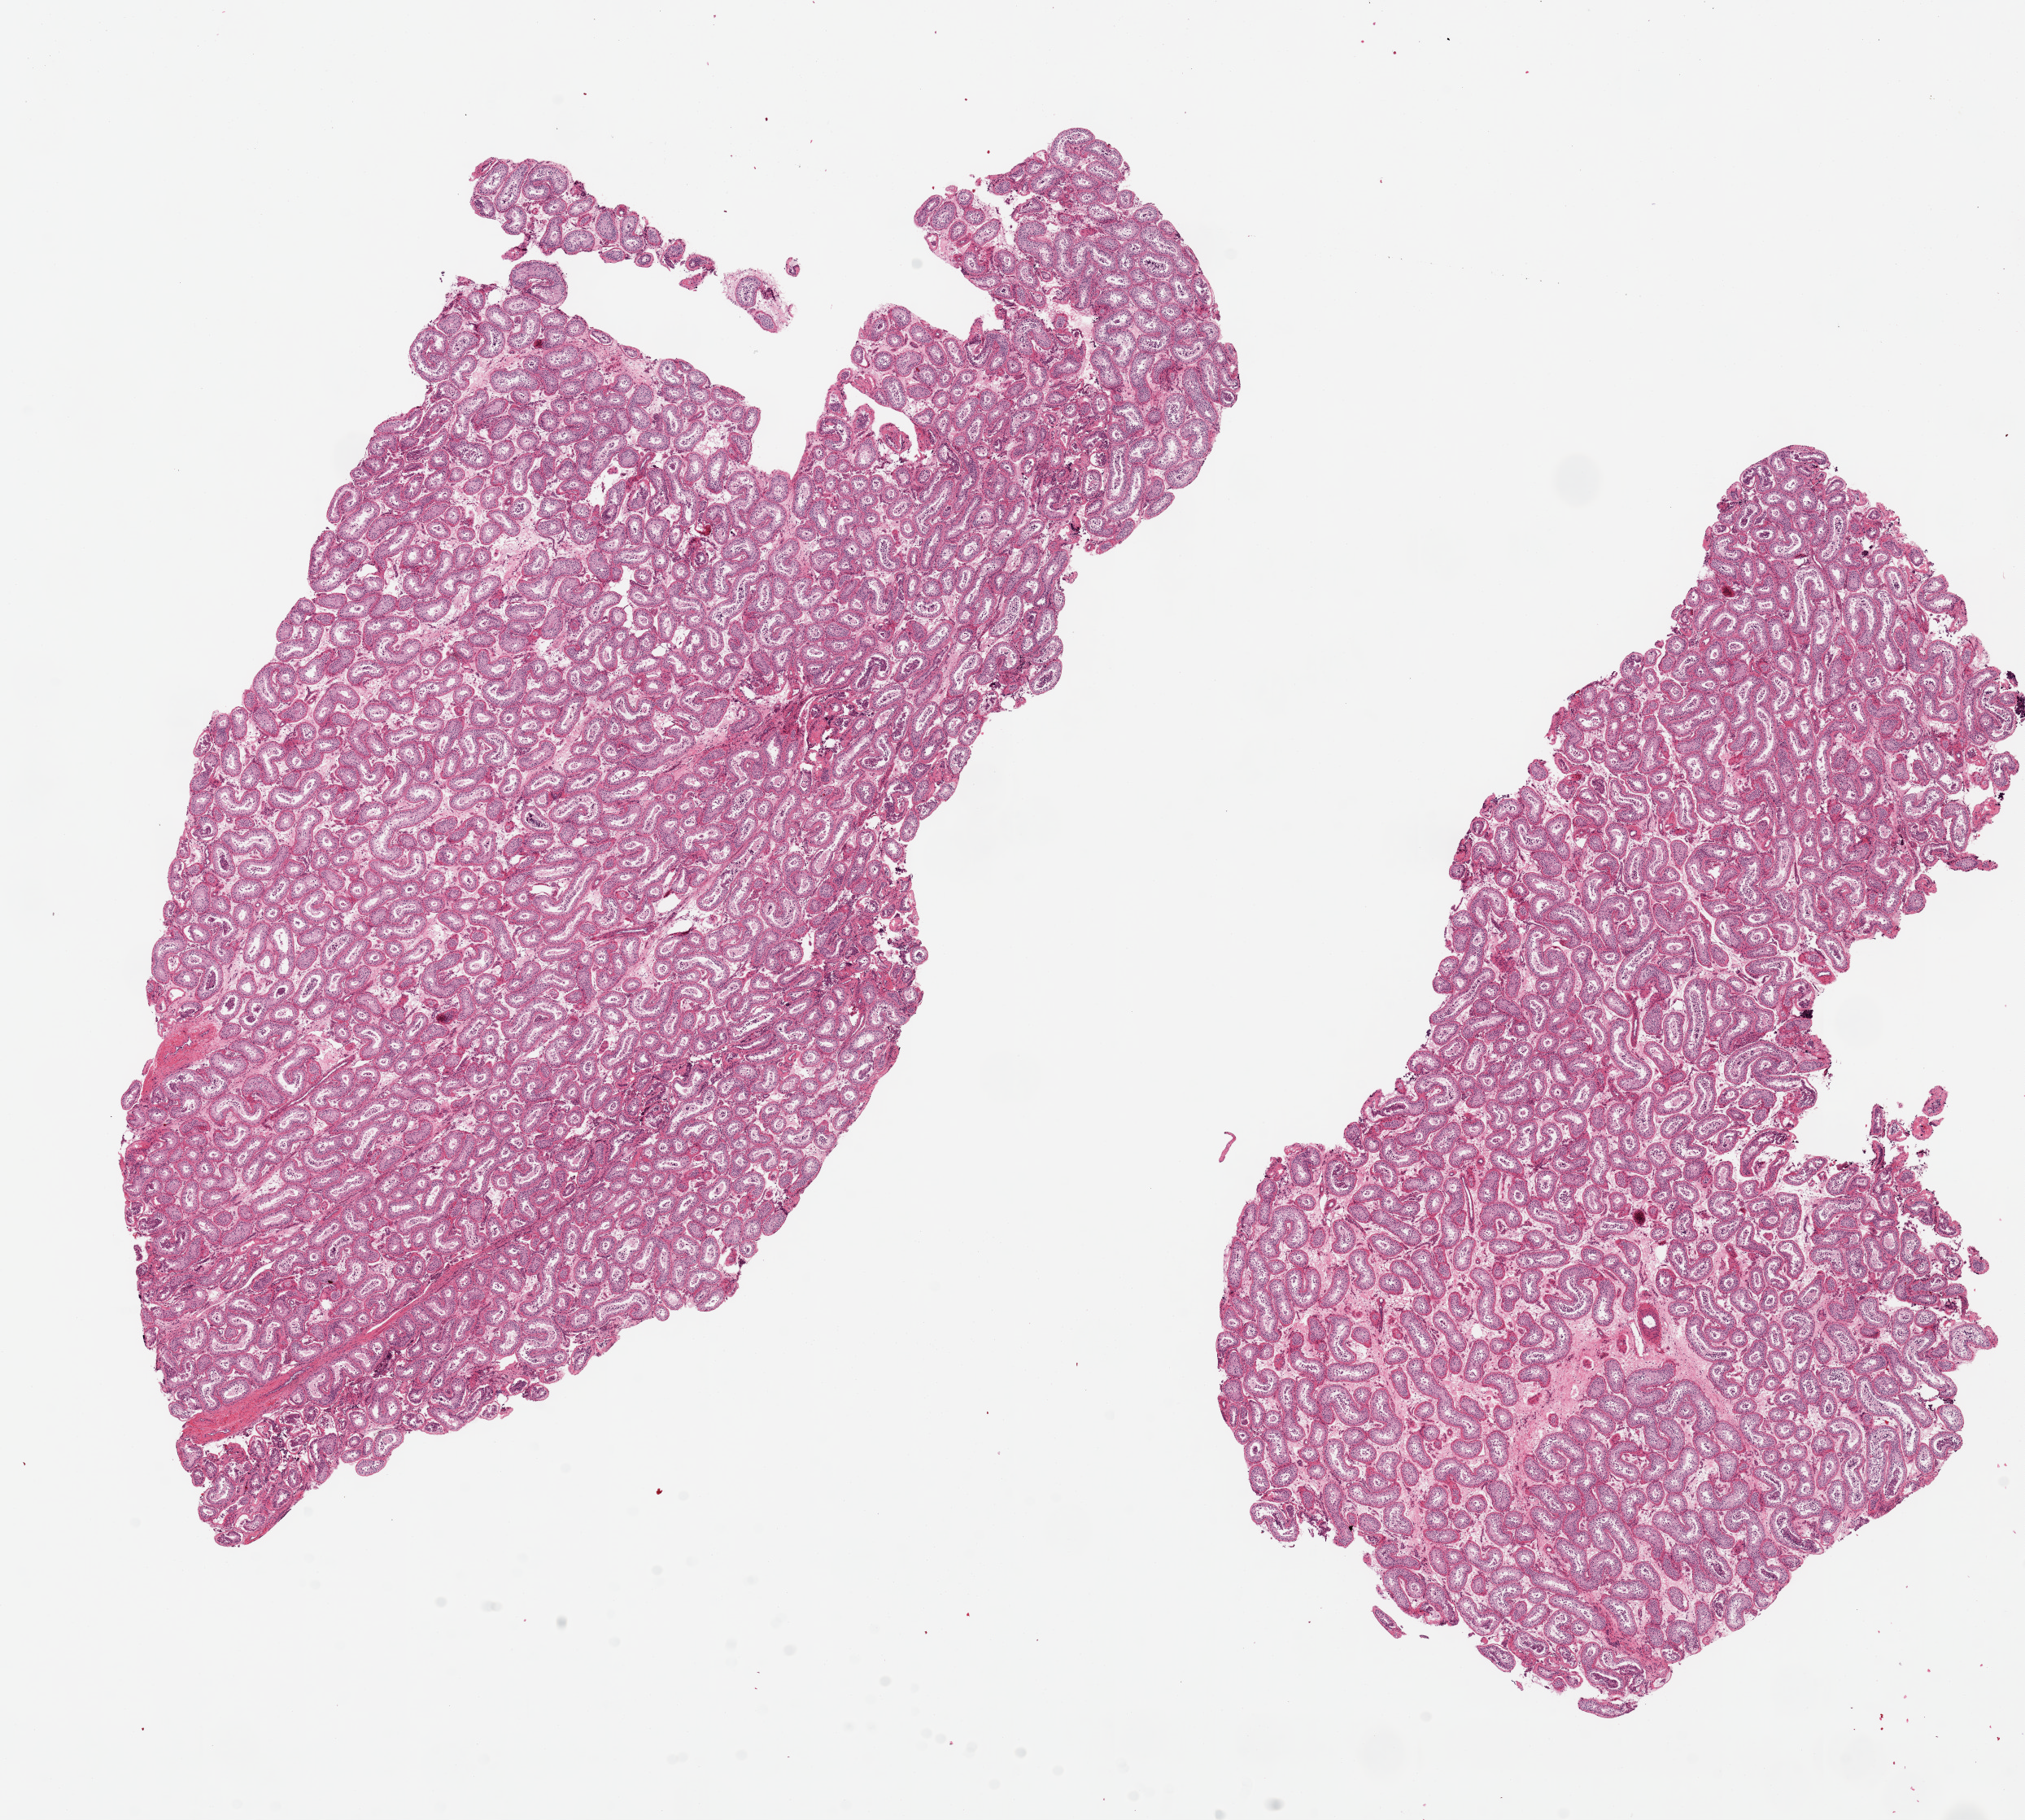
Whole-slide image, haematoxylin and eosin stain — low-resolution overview of the scanned area, about 19.7 x 17.7 mm (slide scanned at 20x); PAXgene-fixed paraffin-embedded (PFPE) section; section of testis (target tissue); tissue donor sample. Donor sex: male.
Review note (as recorded): 2 pieces ~11x7mm. Spermatogenesis is markedly reduced for age of the patient.